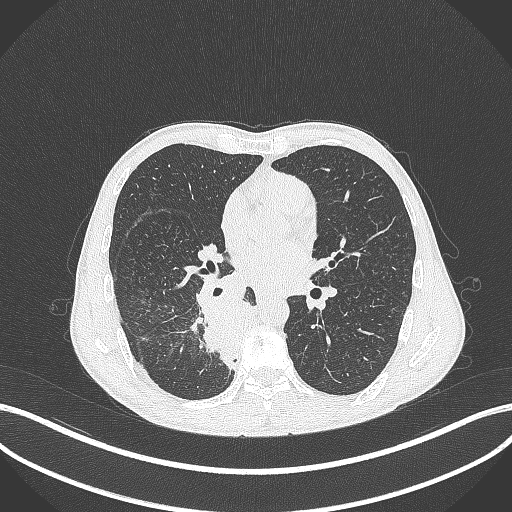
Chest CT, one axial slice. Slice 187 of 371 in the series (ordered by position). Reconstruction kernel B70f. Lung window (W 1500 / L -600 HU). 1 mm slice thickness. 512 × 512 image matrix, field of view 400 × 400 mm. Patient: male, 58 years. From the clinical record (not read from this slice): clinical TNM (as recorded): T3 N1 M1.
Structures marked on this image (bounding box drawn by a radiologist):
- lung tumour (recorded histology: squamous cell carcinoma): bounding box [x1, y1, x2, y2] px = [193, 287, 259, 368]